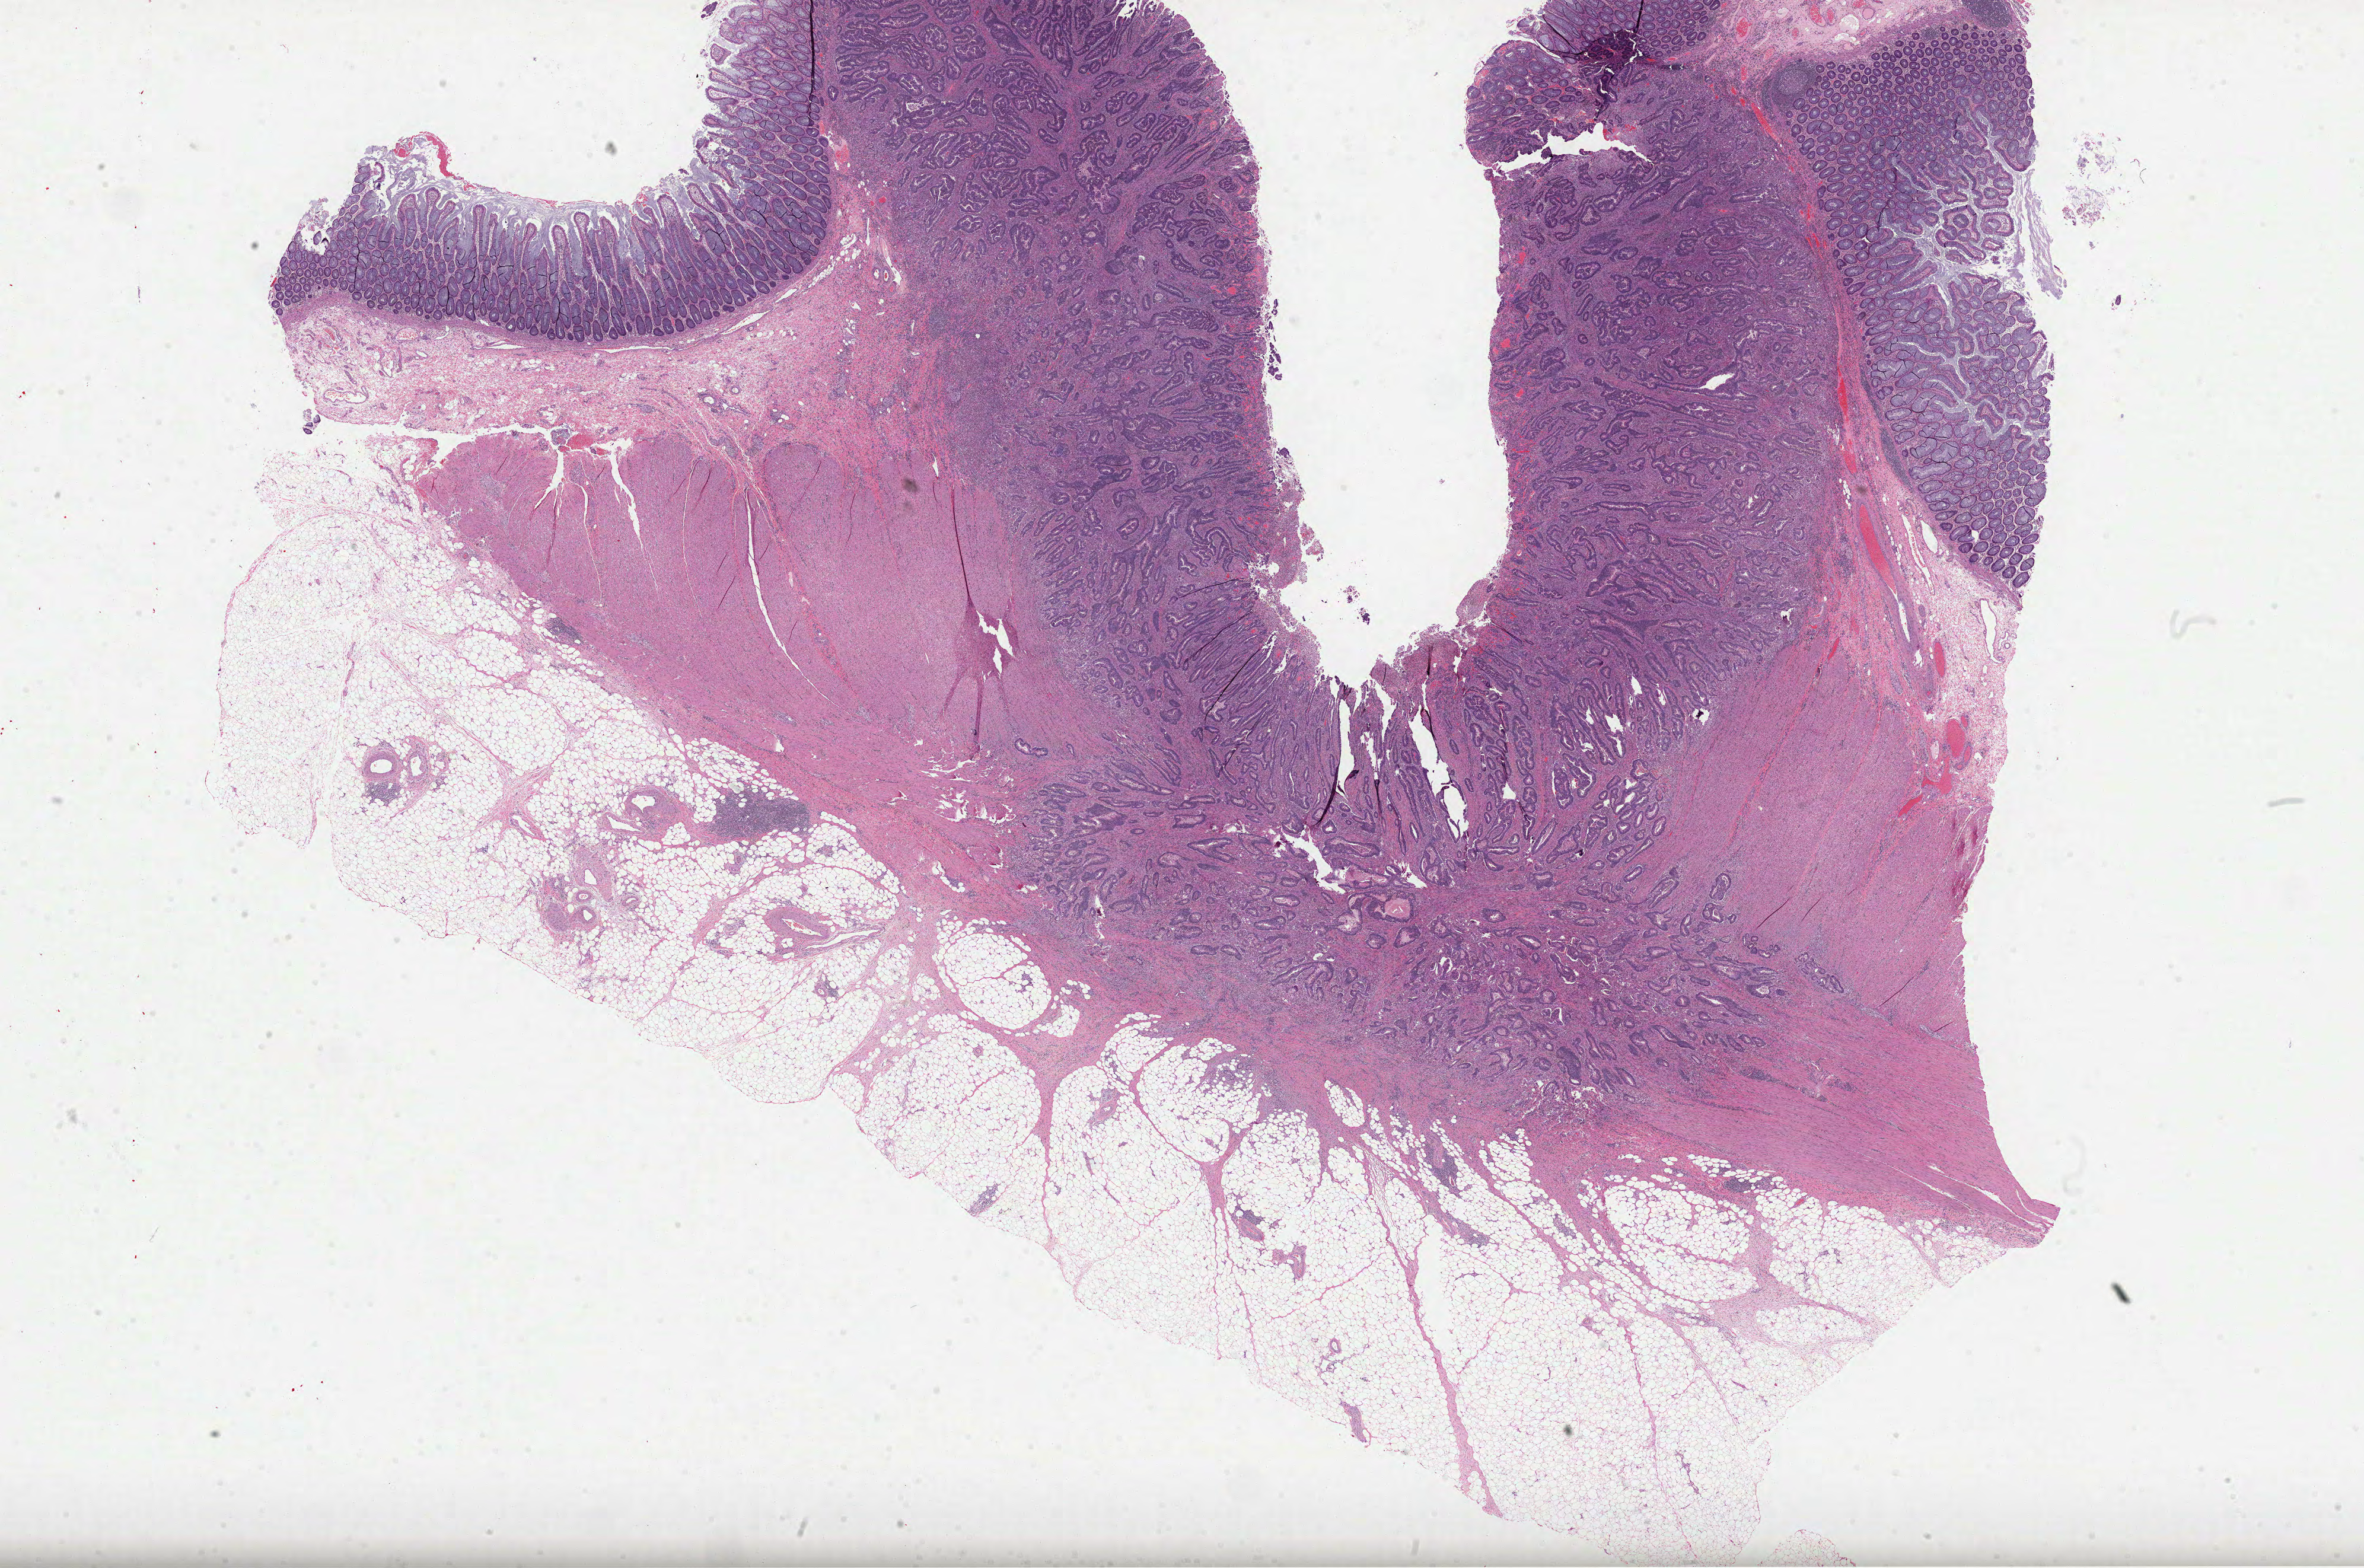
H&E-stained whole-slide image — a low-resolution overview of the entire scanned area, about 32.1 x 21.3 mm (slide scanned at 40x). Formalin-fixed paraffin-embedded (FFPE) diagnostic section. Primary tumour sample from the colon. Male, age 58 years at initial diagnosis.
- pathologic diagnosis: Adenocarcinoma, NOS (sigmoid colon)
- AJCC pathologic stage: IIA (7th edition)
- lymph nodes positive (case pathology): 0 of 21 examined